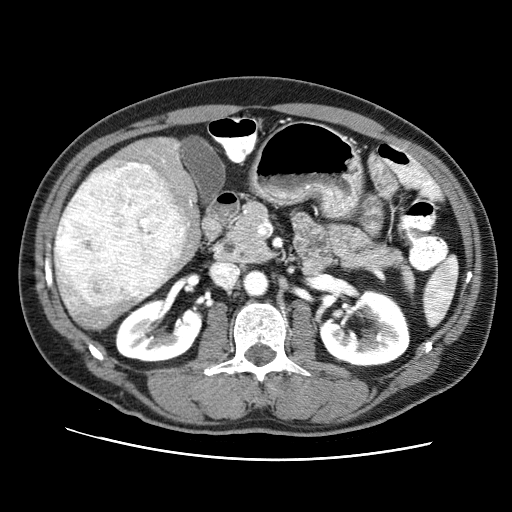
Contrast-enhanced abdominal CT (liver protocol), one axial slice. Slice 33 of 71 in the series (ordered by position). Reconstruction kernel STANDARD. 120 kVp. Soft-tissue window (W 400 / L 40 HU). 2.5 mm slice thickness. 512 × 512 image matrix, field of view 360 × 360 mm. Case-level facts recorded for this patient, not image findings: diagnosis: hepatocellular carcinoma (patient treated with transarterial chemoembolisation; whether this scan precedes or follows treatment is not stated here); TNM stage (as recorded): Stage-II; Child-Pugh class: A; tumour differentiation: well differentiated; tumour nodularity: multinodular.
Annotated regions visible in this slice (semi-automatically segmented with operator editing):
- liver parenchyma outside the tumour (the mass and vessels are separate outlines, so this box may not span the whole liver): bounding box <54,136,200,330> (left, top, right, bottom; pixels)
- mass: <54,158,188,307>
- liver vessels: <61,159,192,313>